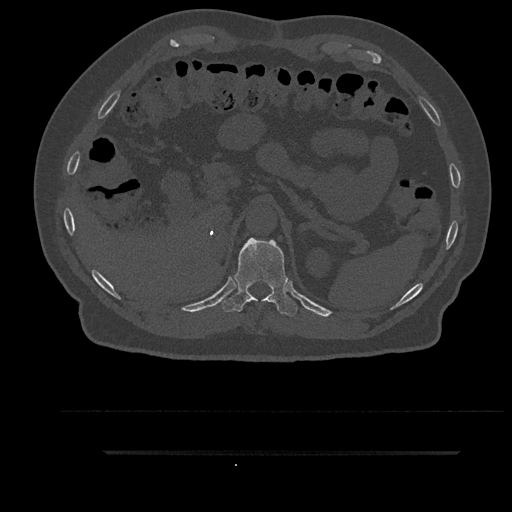
CT including the spine, one axial slice; slice 312 of 797 in the series (ordered by position); reconstruction kernel Br40s/3; 120 kVp; bone window (W 1800 / L 400 HU); 0.5 mm slice thickness; 512 × 512 image matrix, field of view 432 × 432 mm. Patient: male, 63 years. Case-level facts recorded for this patient, not image findings: primary cancer: renal; vertebrae with lytic lesions (as recorded): T8.
Outlined on this slice (semi-automatically segmented with operator editing):
- T11 vertebra: box from (x=221, y=238) to (x=298, y=316) px